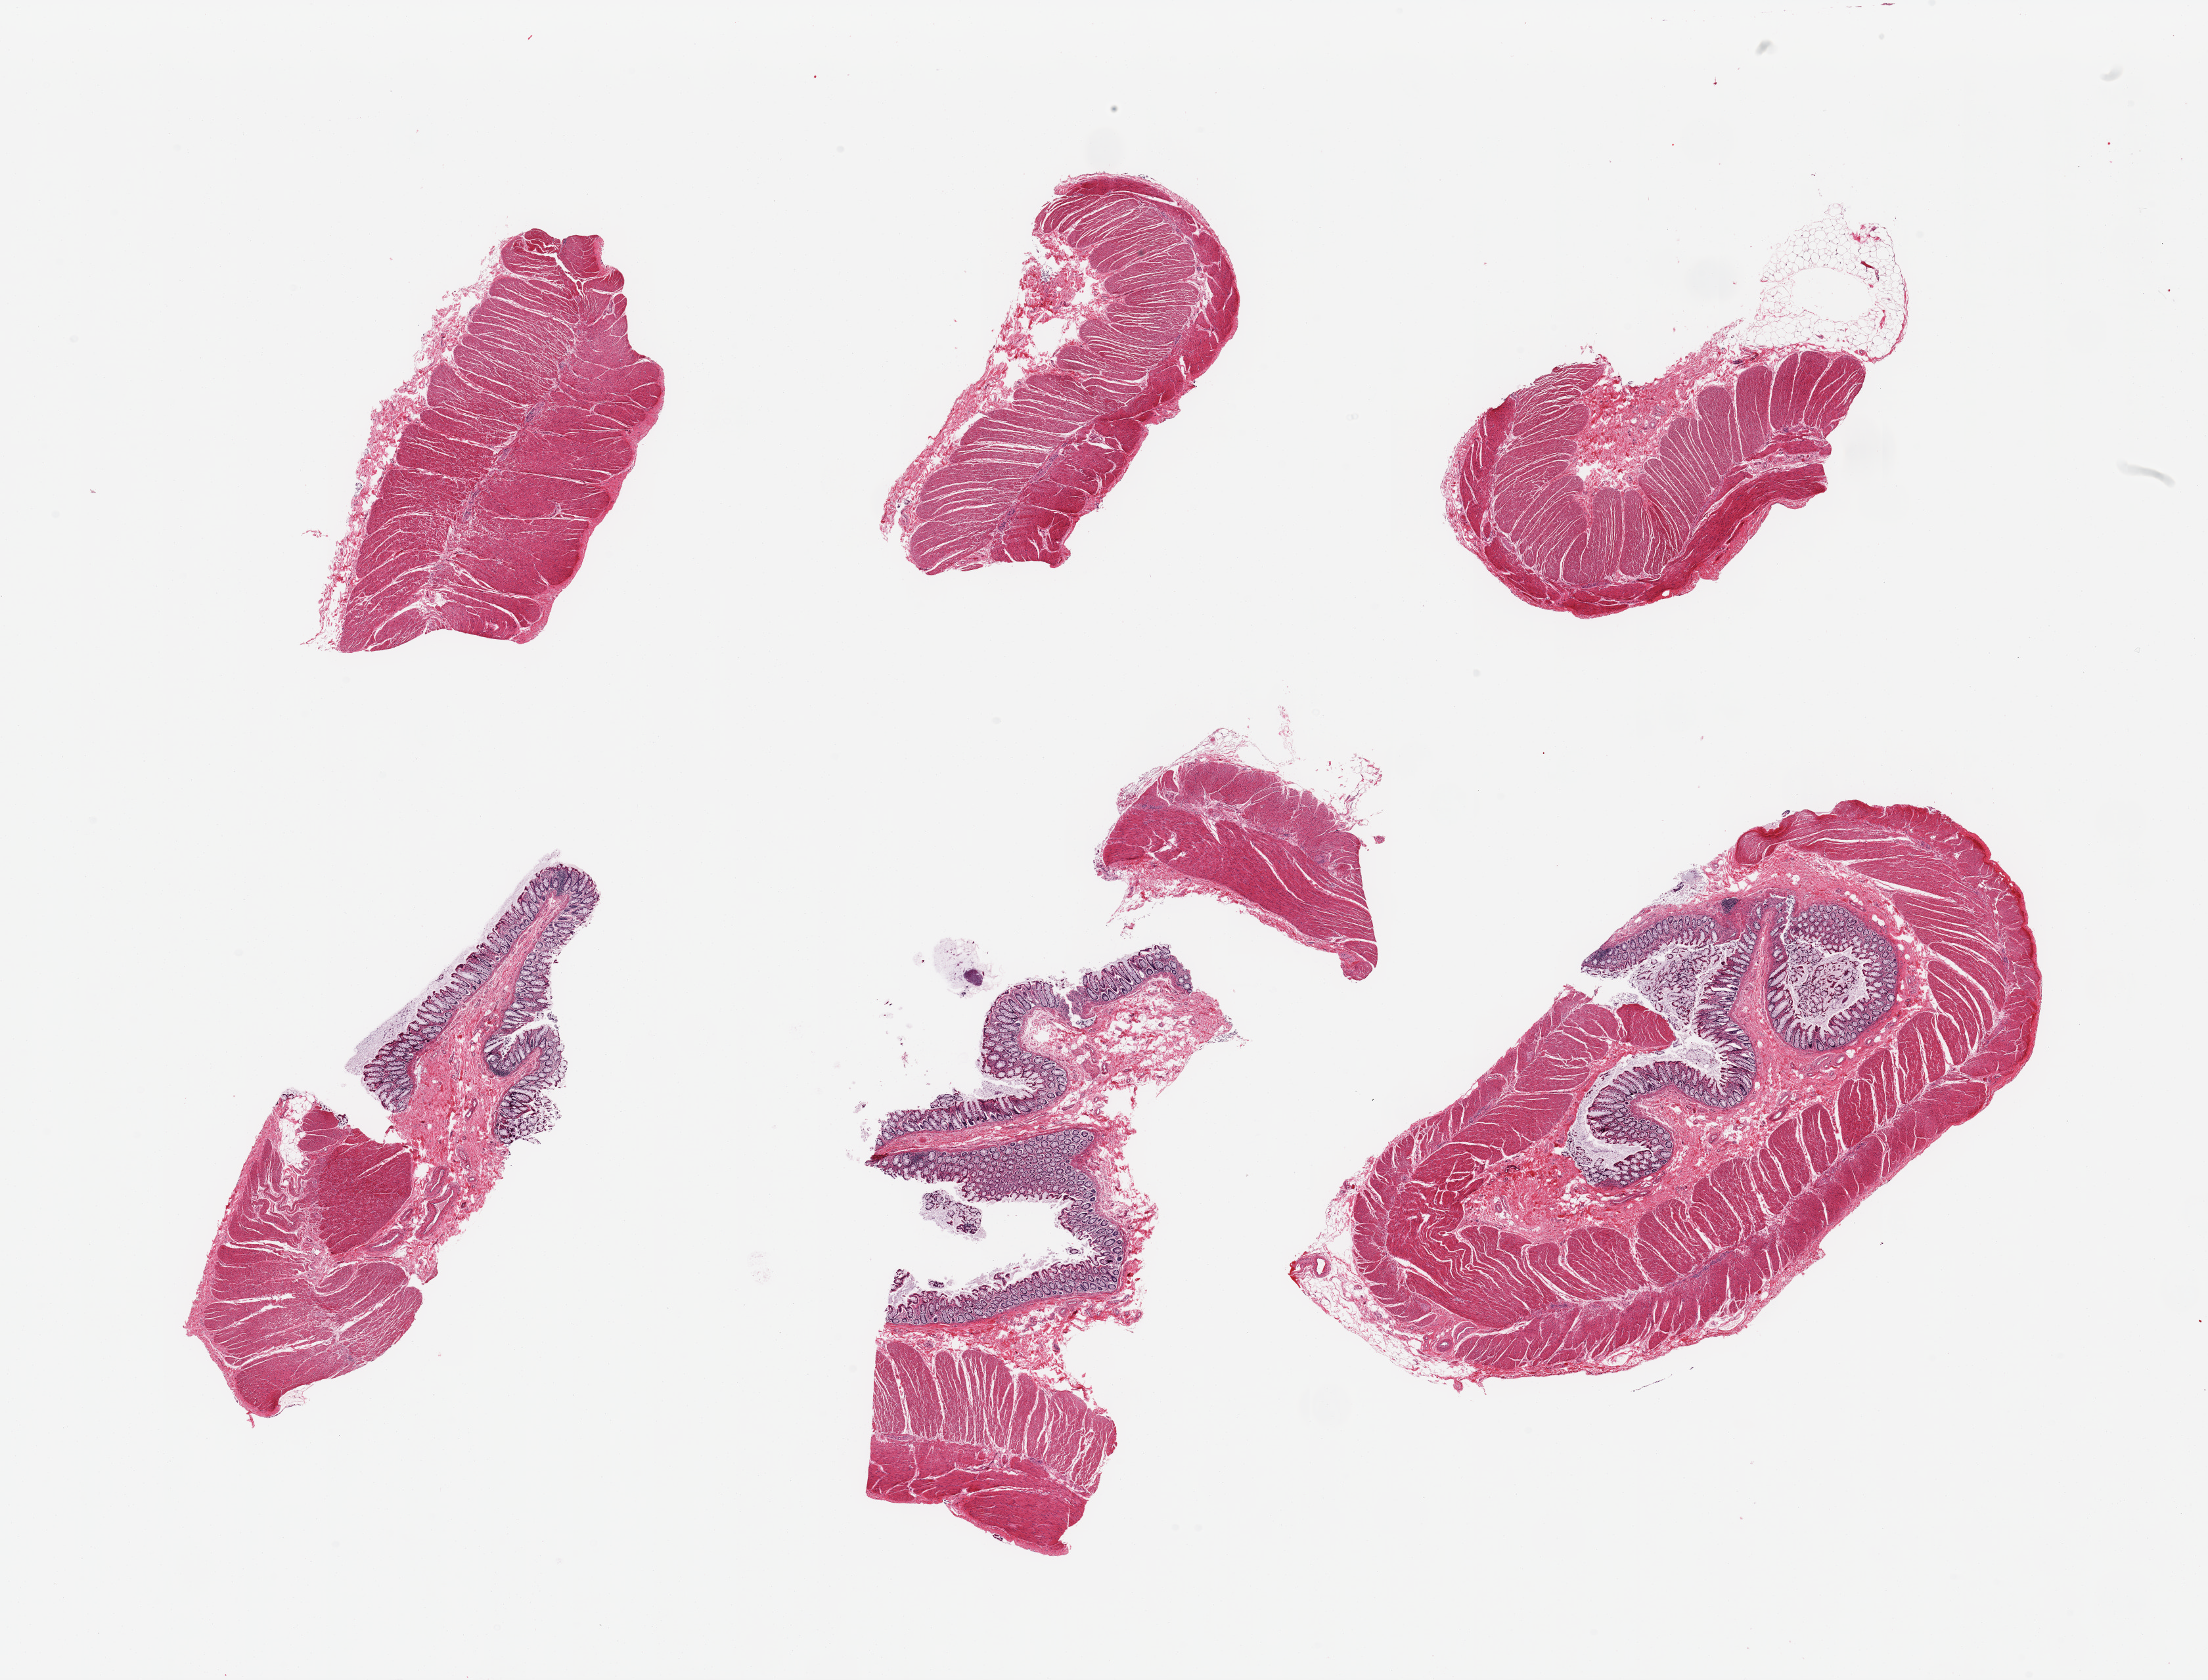
Whole-slide image, H&E stain, brightfield, low-resolution overview of the scanned area, about 26.6 x 20.2 mm (slide scanned at 20x); PAXgene-fixed paraffin-embedded (PFPE) section; sampled site (target tissue): sigmoid colon; donor tissue sample. Donor: male.
Review note (as recorded): 6 pieces, mainly muscularis, ~20% 'contaminant' mucosa.